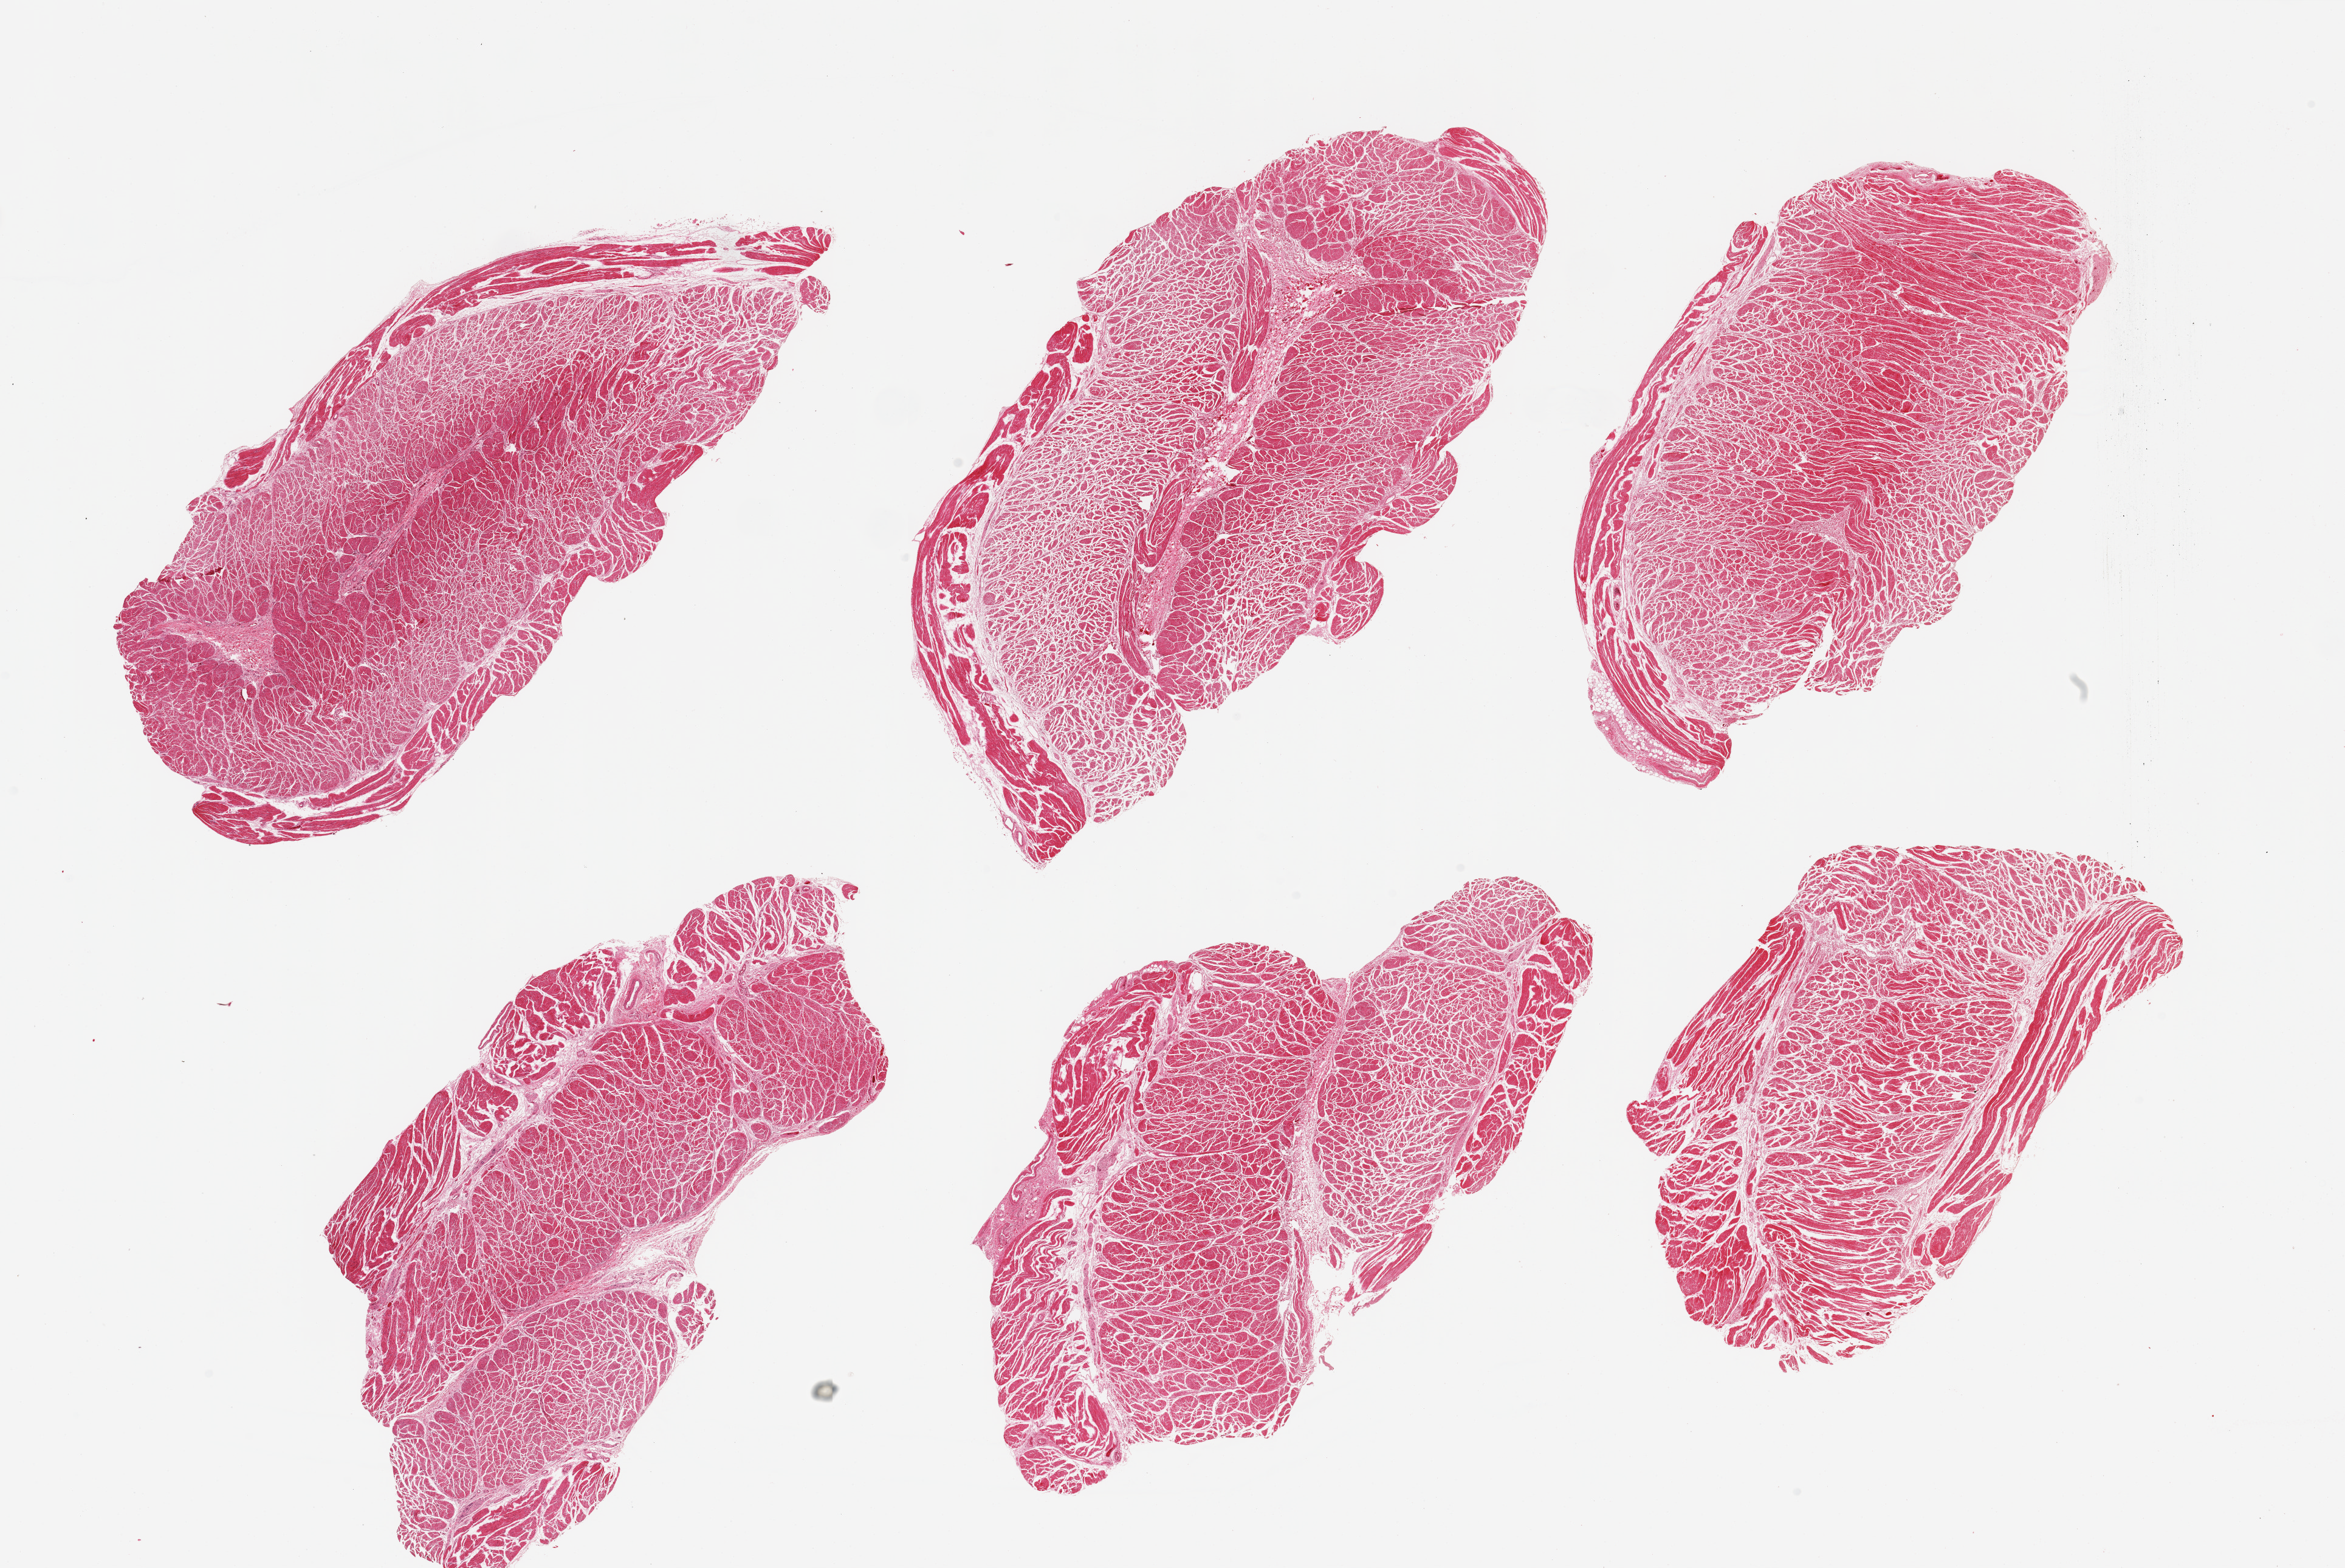
Haematoxylin and eosin whole-slide image, shown as a low-resolution overview of the whole scanned area (about 30.5 x 20.4 mm), PAXgene-fixed paraffin-embedded (PFPE) section, sampled site (target tissue): esophageal muscle, tissue donor sample. Donor: male.
Pathologist's review note for this sample: 6 pieces; well trimmed.